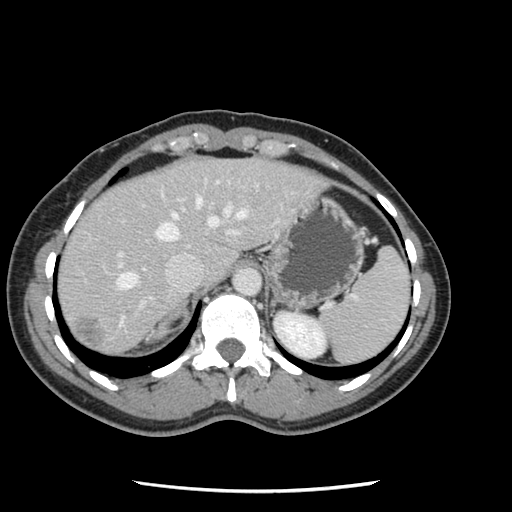
Contrast-enhanced abdominal CT, one axial slice. Position 95 of 134 along the scan axis. Intravenous contrast given. Soft-tissue window (W 400 / L 40 HU). 2.5 mm slice thickness. 512 × 512 image matrix, field of view 330 × 330 mm. Female patient, age 43 years. Case-level facts recorded for this patient, not image findings: diagnosis: colorectal cancer liver metastases, imaged before liver resection; multiple liver metastases: yes; largest metastasis: 3.4 cm; disease in both lobes: yes.
Structures marked on this image (manually delineated by an expert):
- hepatic veins: bounding box <116,196,248,324> (left, top, right, bottom; pixels)
- liver: <58,158,322,356>
- planned liver remnant (the part of the liver to remain after resection): <59,166,194,309>
- portal vein (with intrahepatic branches): <117,181,240,310>
- liver metastasis: <73,318,103,350>